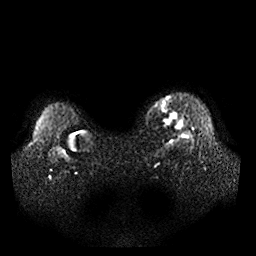
Breast MRI, one axial slice. Position 30 of 32 along the scan axis. Diffusion-weighted series; image 2 of 4 stored at this slice position (different b-values; order by instance number). 1.5 T. 4 mm slice thickness. 256 × 256 image matrix, field of view 360 × 360 mm. Female patient.
Annotated regions visible in this slice (expert manual segmentation):
- tumour on diffusion-weighted imaging: bounding box [x1, y1, x2, y2] px = [165, 112, 185, 130]